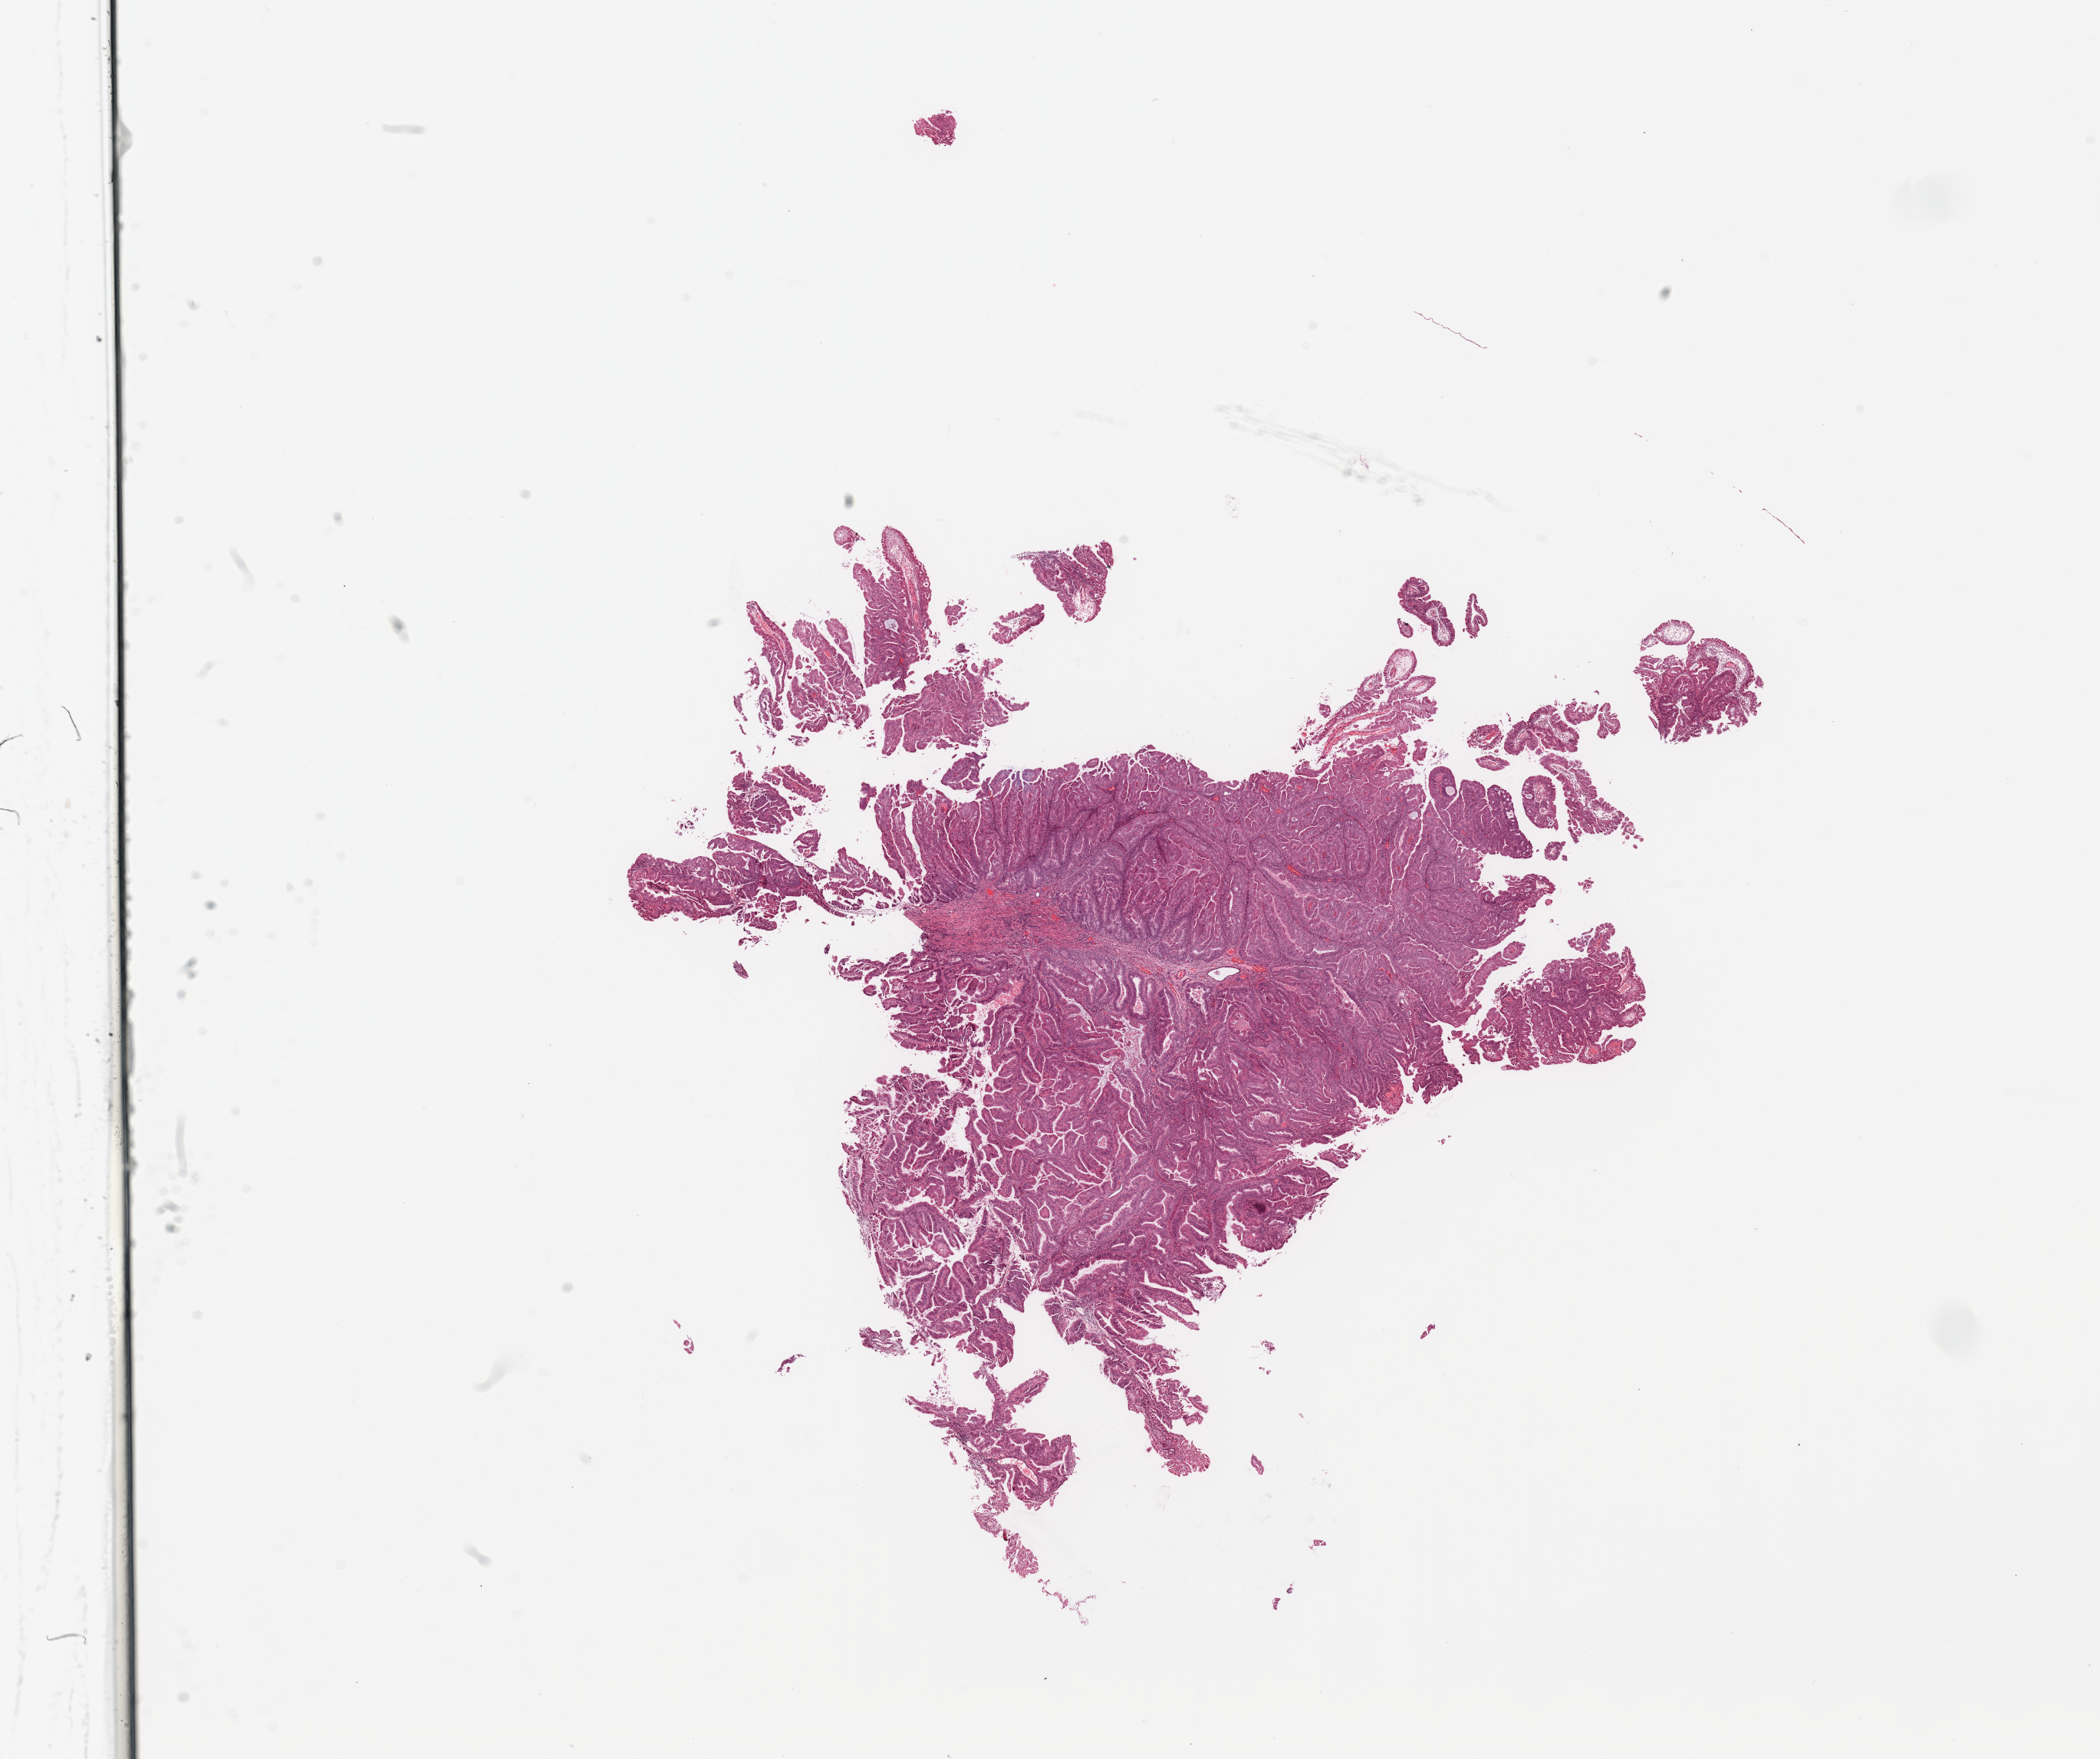
Whole-slide histology image, H&E-stained — a low-resolution overview of the entire scanned area, about 21.7 x 18.1 mm; tumour tissue sample, uterus. Patient: female, age 66 years. Histologic grade: G2 (moderately differentiated).
Histologic diagnosis: Endometrioid adenocarcinoma, NOS. AJCC pathologic stage: IB.